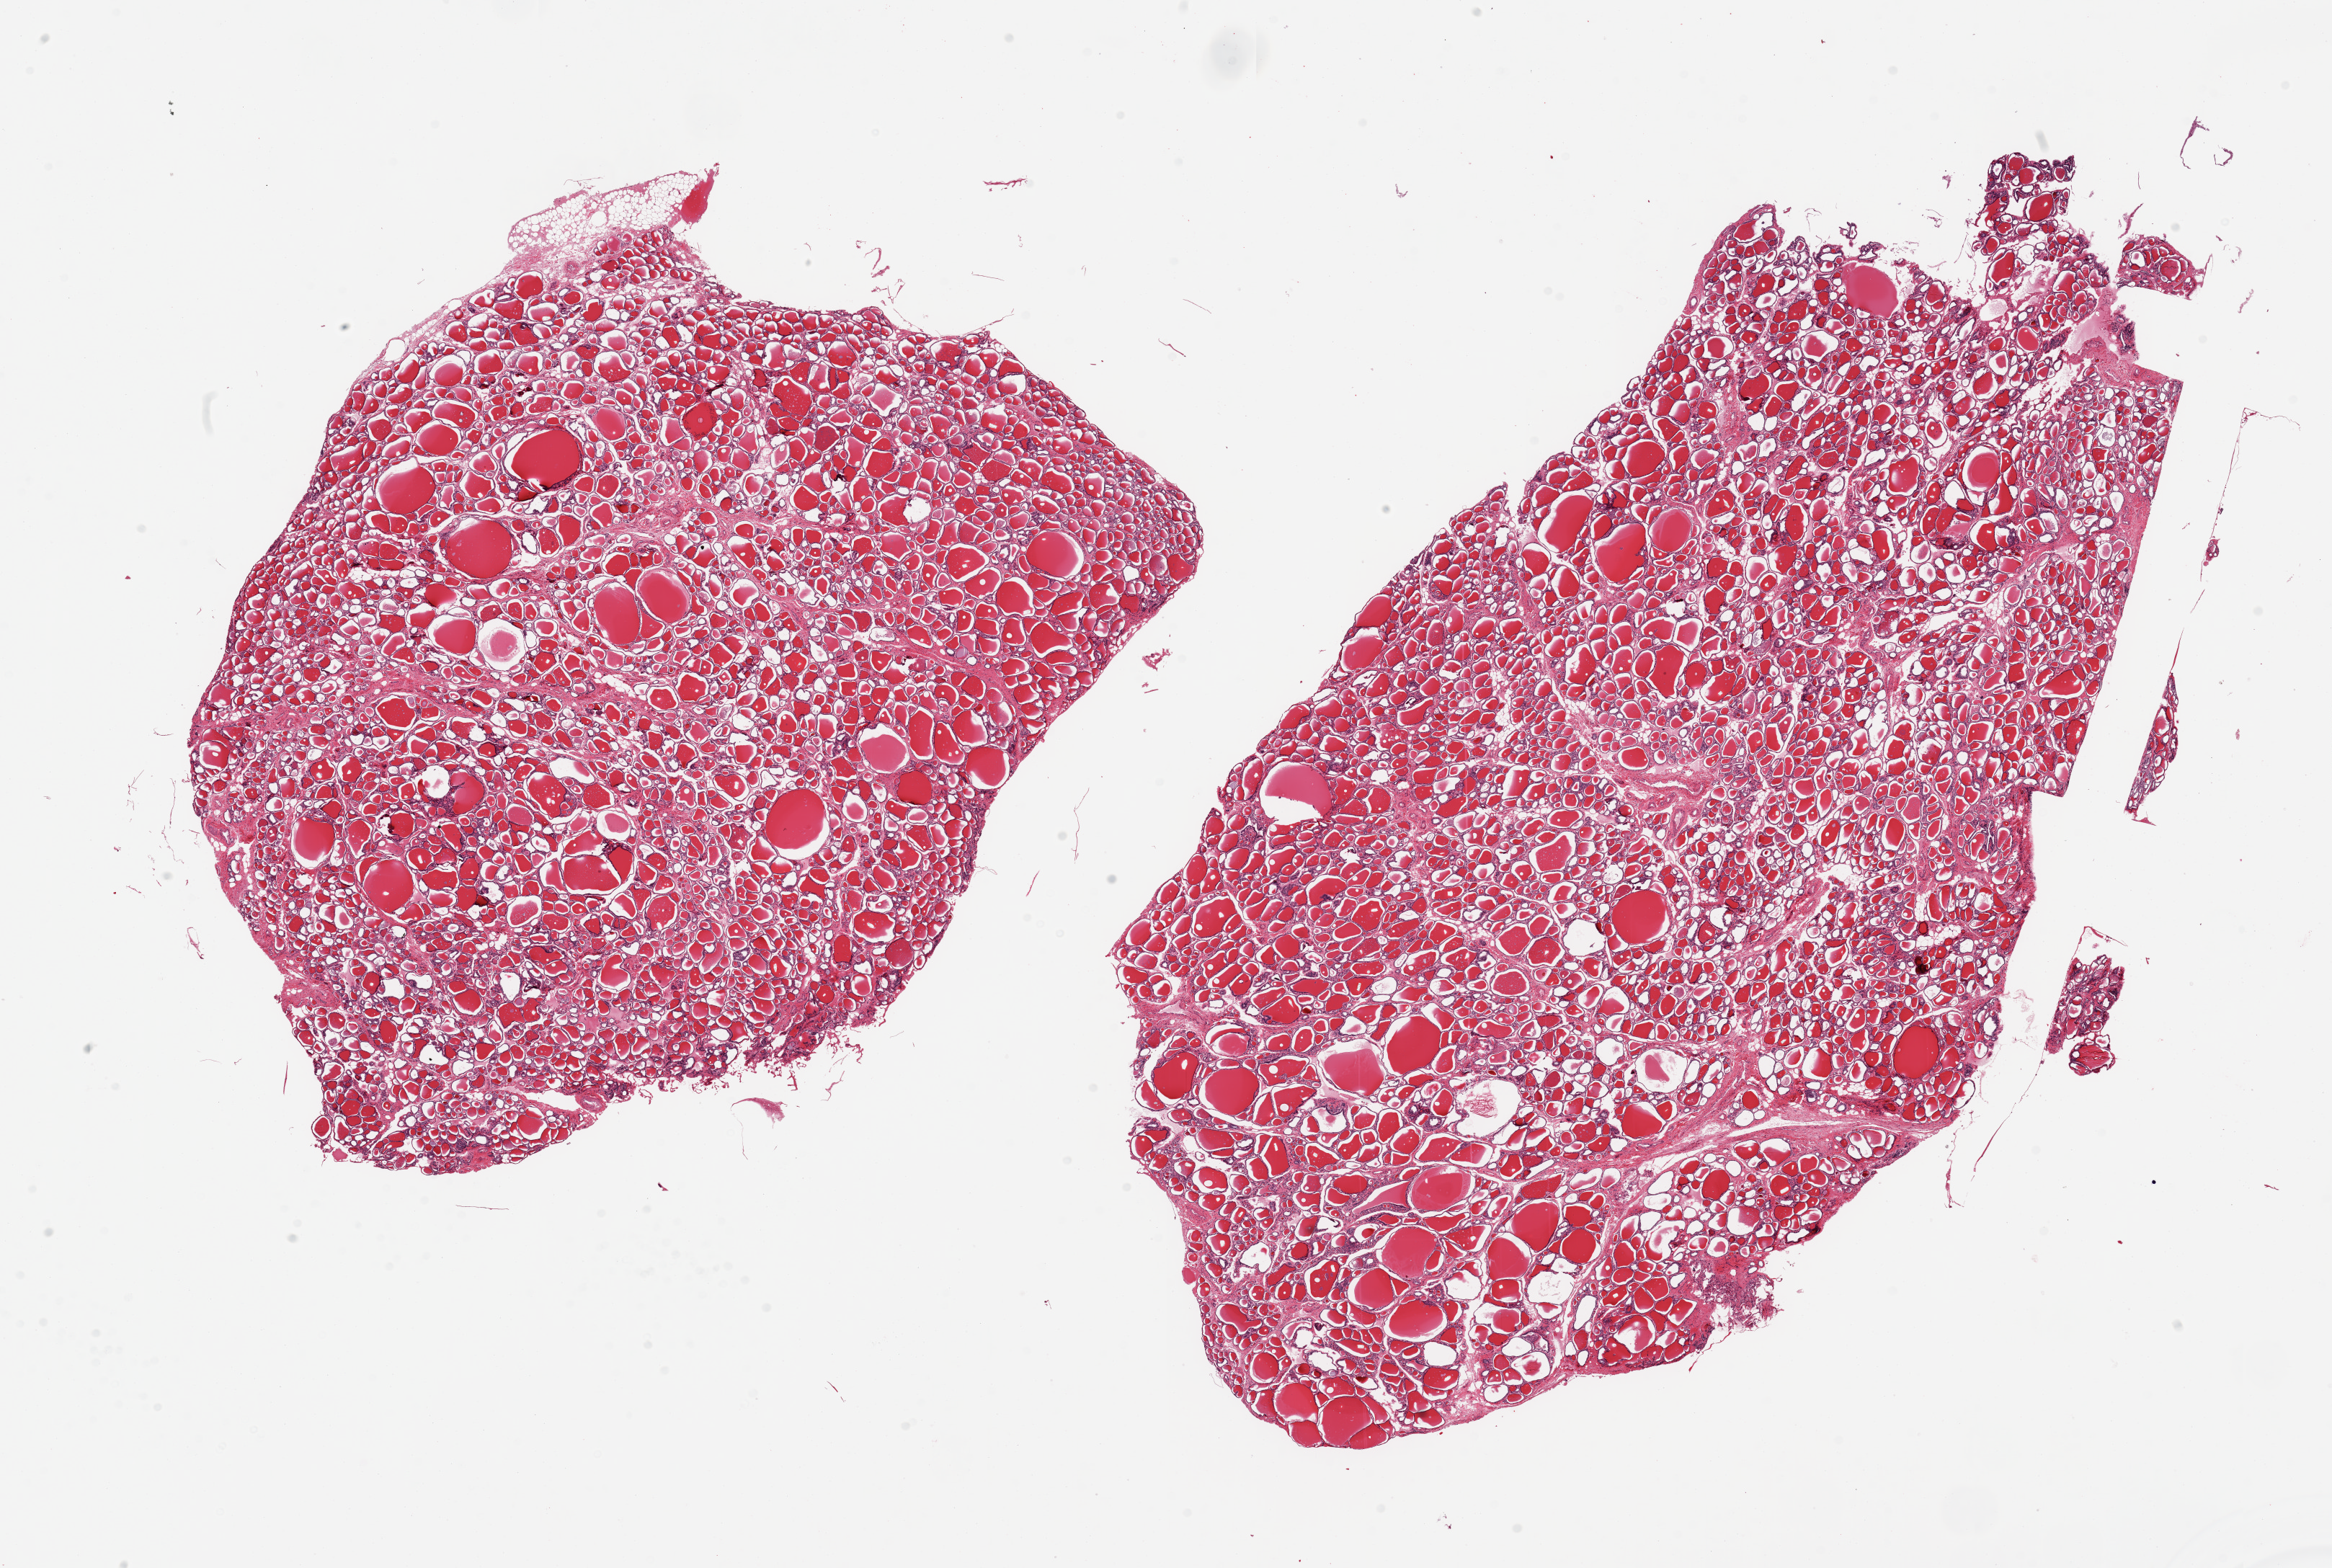
H&E whole-slide image, brightfield — a low-resolution overview of the entire scanned area, about 25.6 x 17.2 mm (from a 20x scan); PAXgene-fixed paraffin-embedded (PFPE) section; sampled site (target tissue): thyroid; donor tissue sample. Donor sex: female.
• pathologist's review note for this sample: 2 pieces, no abnormalities